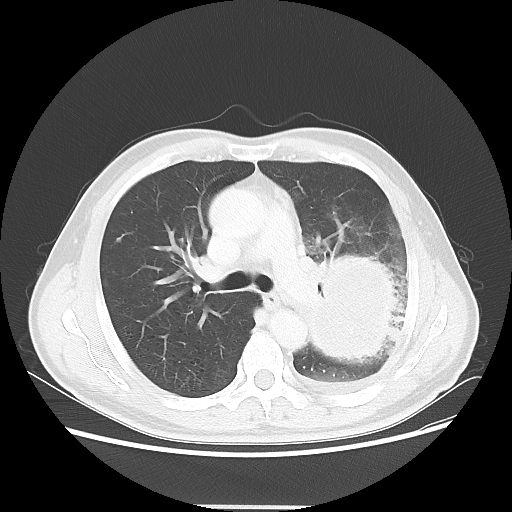
Chest CT, one axial slice. Slice 34 of 53 in the series (ordered by position). Reconstruction kernel LUNG. 100 kVp. Lung window (W 1500 / L -600 HU). 512 × 512 image matrix, field of view 391 × 391 mm. Male patient, age 60 years. From the clinical record (not read from this slice): clinical TNM (as recorded): T4 N1 M1a.
Annotated regions visible in this slice (bounding box drawn by a radiologist):
- lung tumour (recorded histology: large cell carcinoma): bounding box (x1, y1, x2, y2) in pixels: (289, 227, 416, 377)